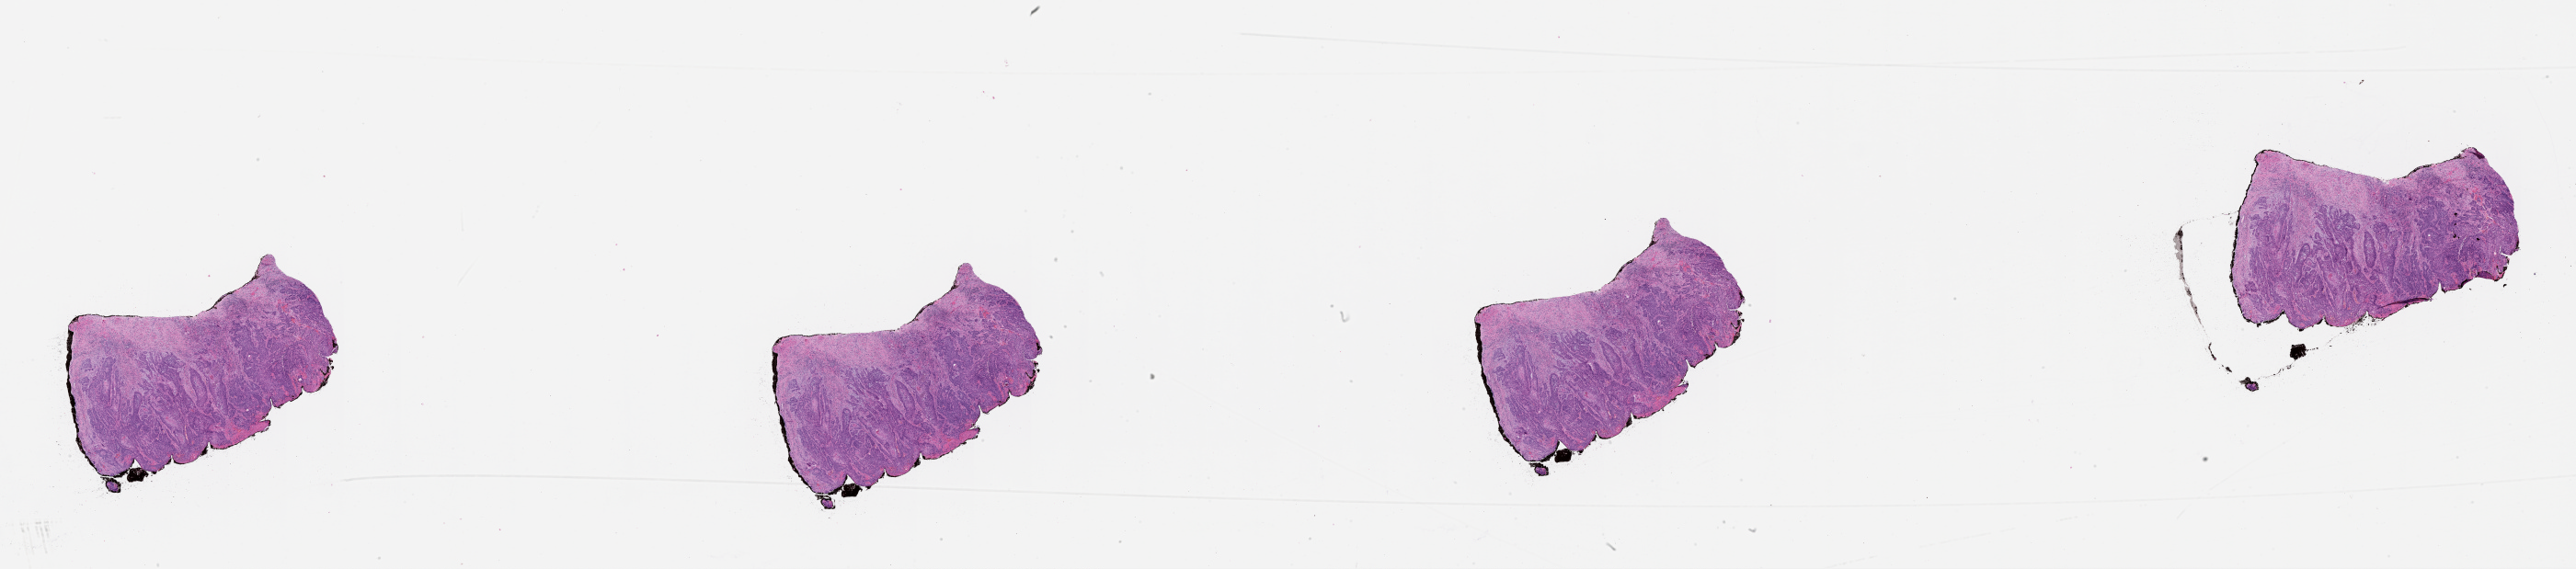
Whole-slide histology image, Hematoxylin and eosin (H&E) stained — a low-resolution overview of the entire scanned area, about 45.1 x 10.0 mm (slide scanned at 20x), tumour tissue sample, sampled site: floor of mouth. Patient: male, age 63 years.
Diagnosis: Squamous cell carcinoma, NOS (floor of mouth, NOS).